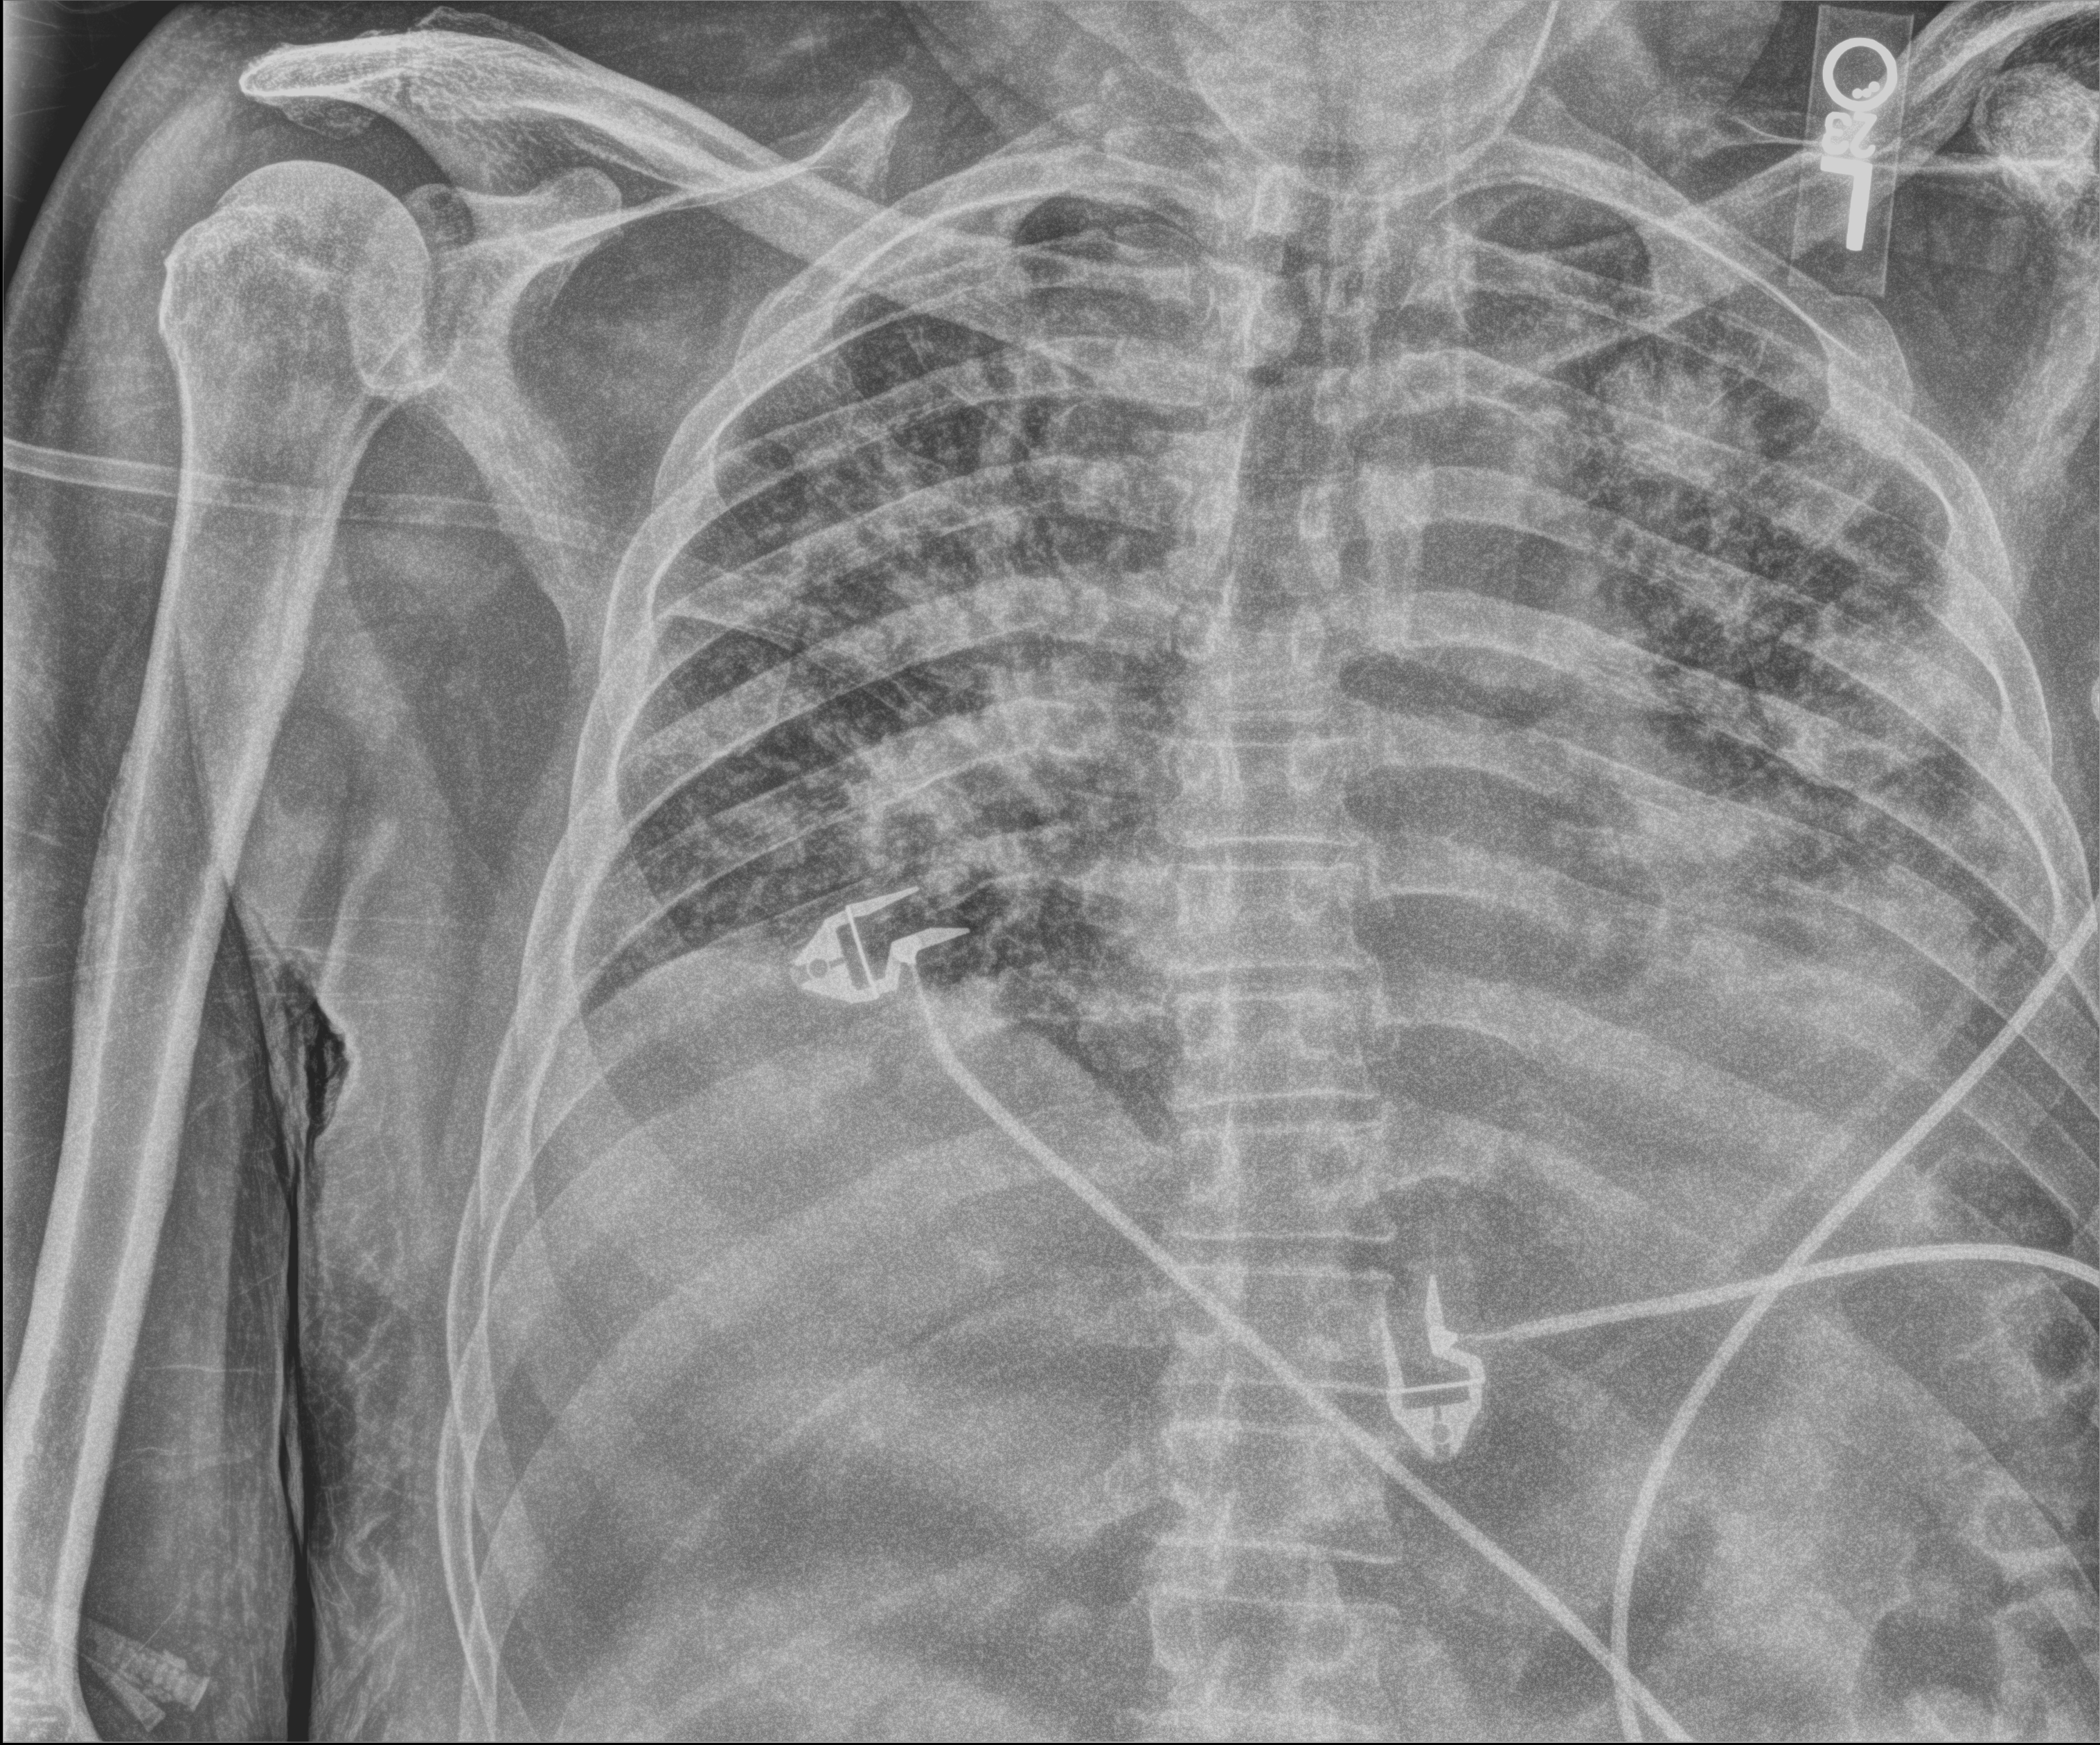
Bedside chest radiograph (computed radiography), anteroposterior (AP) projection. Male patient hospitalised with COVID-19, age 60–74 years.
Hospital-stay facts (about this admission, not read from this image; timing relative to this image not recorded):
- hypertension (admission record): yes
- admitted to intensive care during this hospital stay: no
- mechanically ventilated during this hospital stay: no